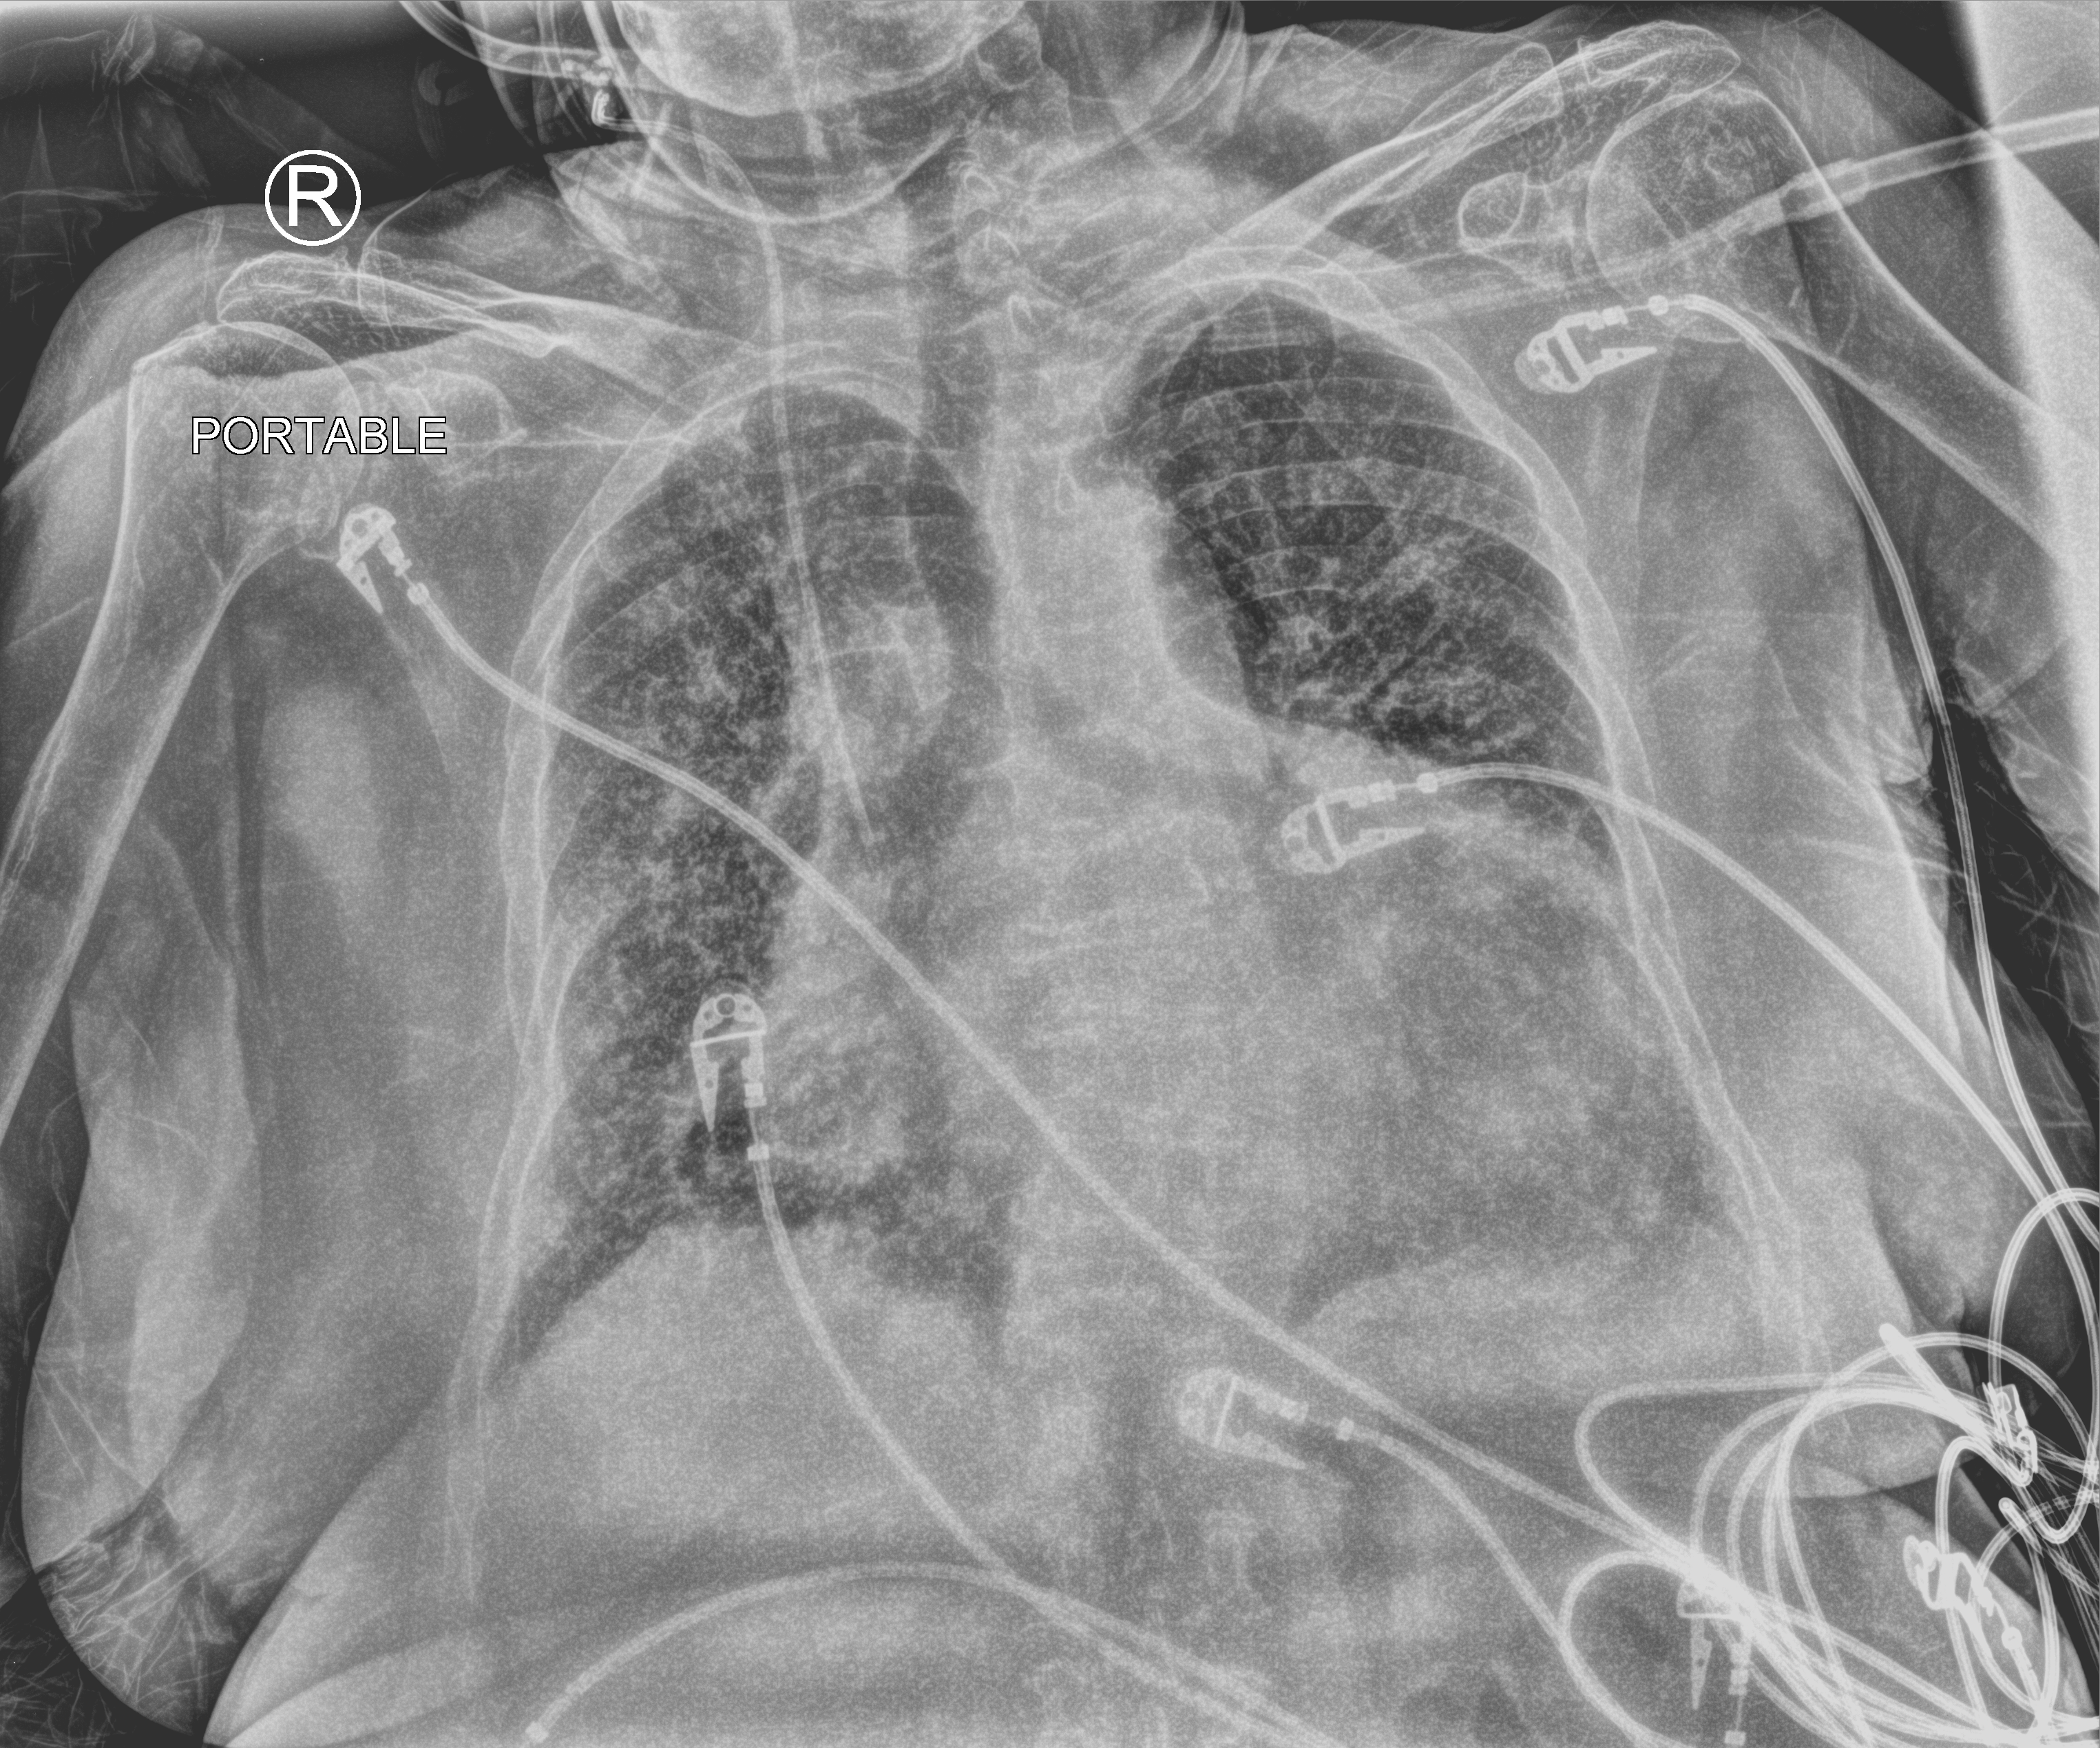
Chest X-ray (portable); anteroposterior (AP) projection. Female patient hospitalised with COVID-19, age 75–90 years.
Admission-level facts for this patient (not findings on this image; timing relative to this image not recorded): other chronic lung disease (admission record): no; admitted to intensive care during this hospital stay: no; mechanically ventilated during this hospital stay: no.